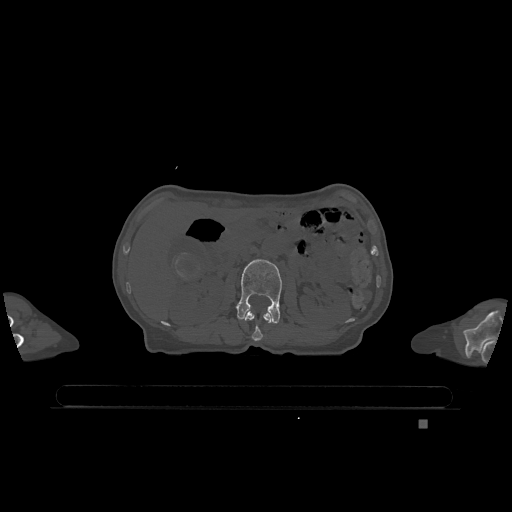
CT including the spine, one axial slice; position 433 of 1317 along the scan axis; bone window (W 1800 / L 400 HU); 0.5 mm slice thickness; 512 × 512 image matrix, field of view 500 × 500 mm. Female patient, age 74 years. From the clinical record (not read from this slice): primary cancer: lung.
Structures marked on this image (semi-automatically segmented with operator editing):
- L1 vertebra: bounding box [x1, y1, x2, y2] px = [244, 311, 272, 341]
- L2 vertebra: [237, 259, 282, 323]